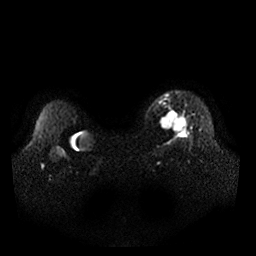
Breast MRI, one axial slice. Diffusion-weighted series; image 2 of 4 stored at this slice position (different b-values; order by instance number). 1.5 T. 256 × 256 image matrix, field of view 360 × 360 mm. Female patient.
Annotated regions visible in this slice (manually delineated by an expert):
- tumour on diffusion-weighted imaging: bounding box [x1, y1, x2, y2] px = [160, 110, 187, 132]